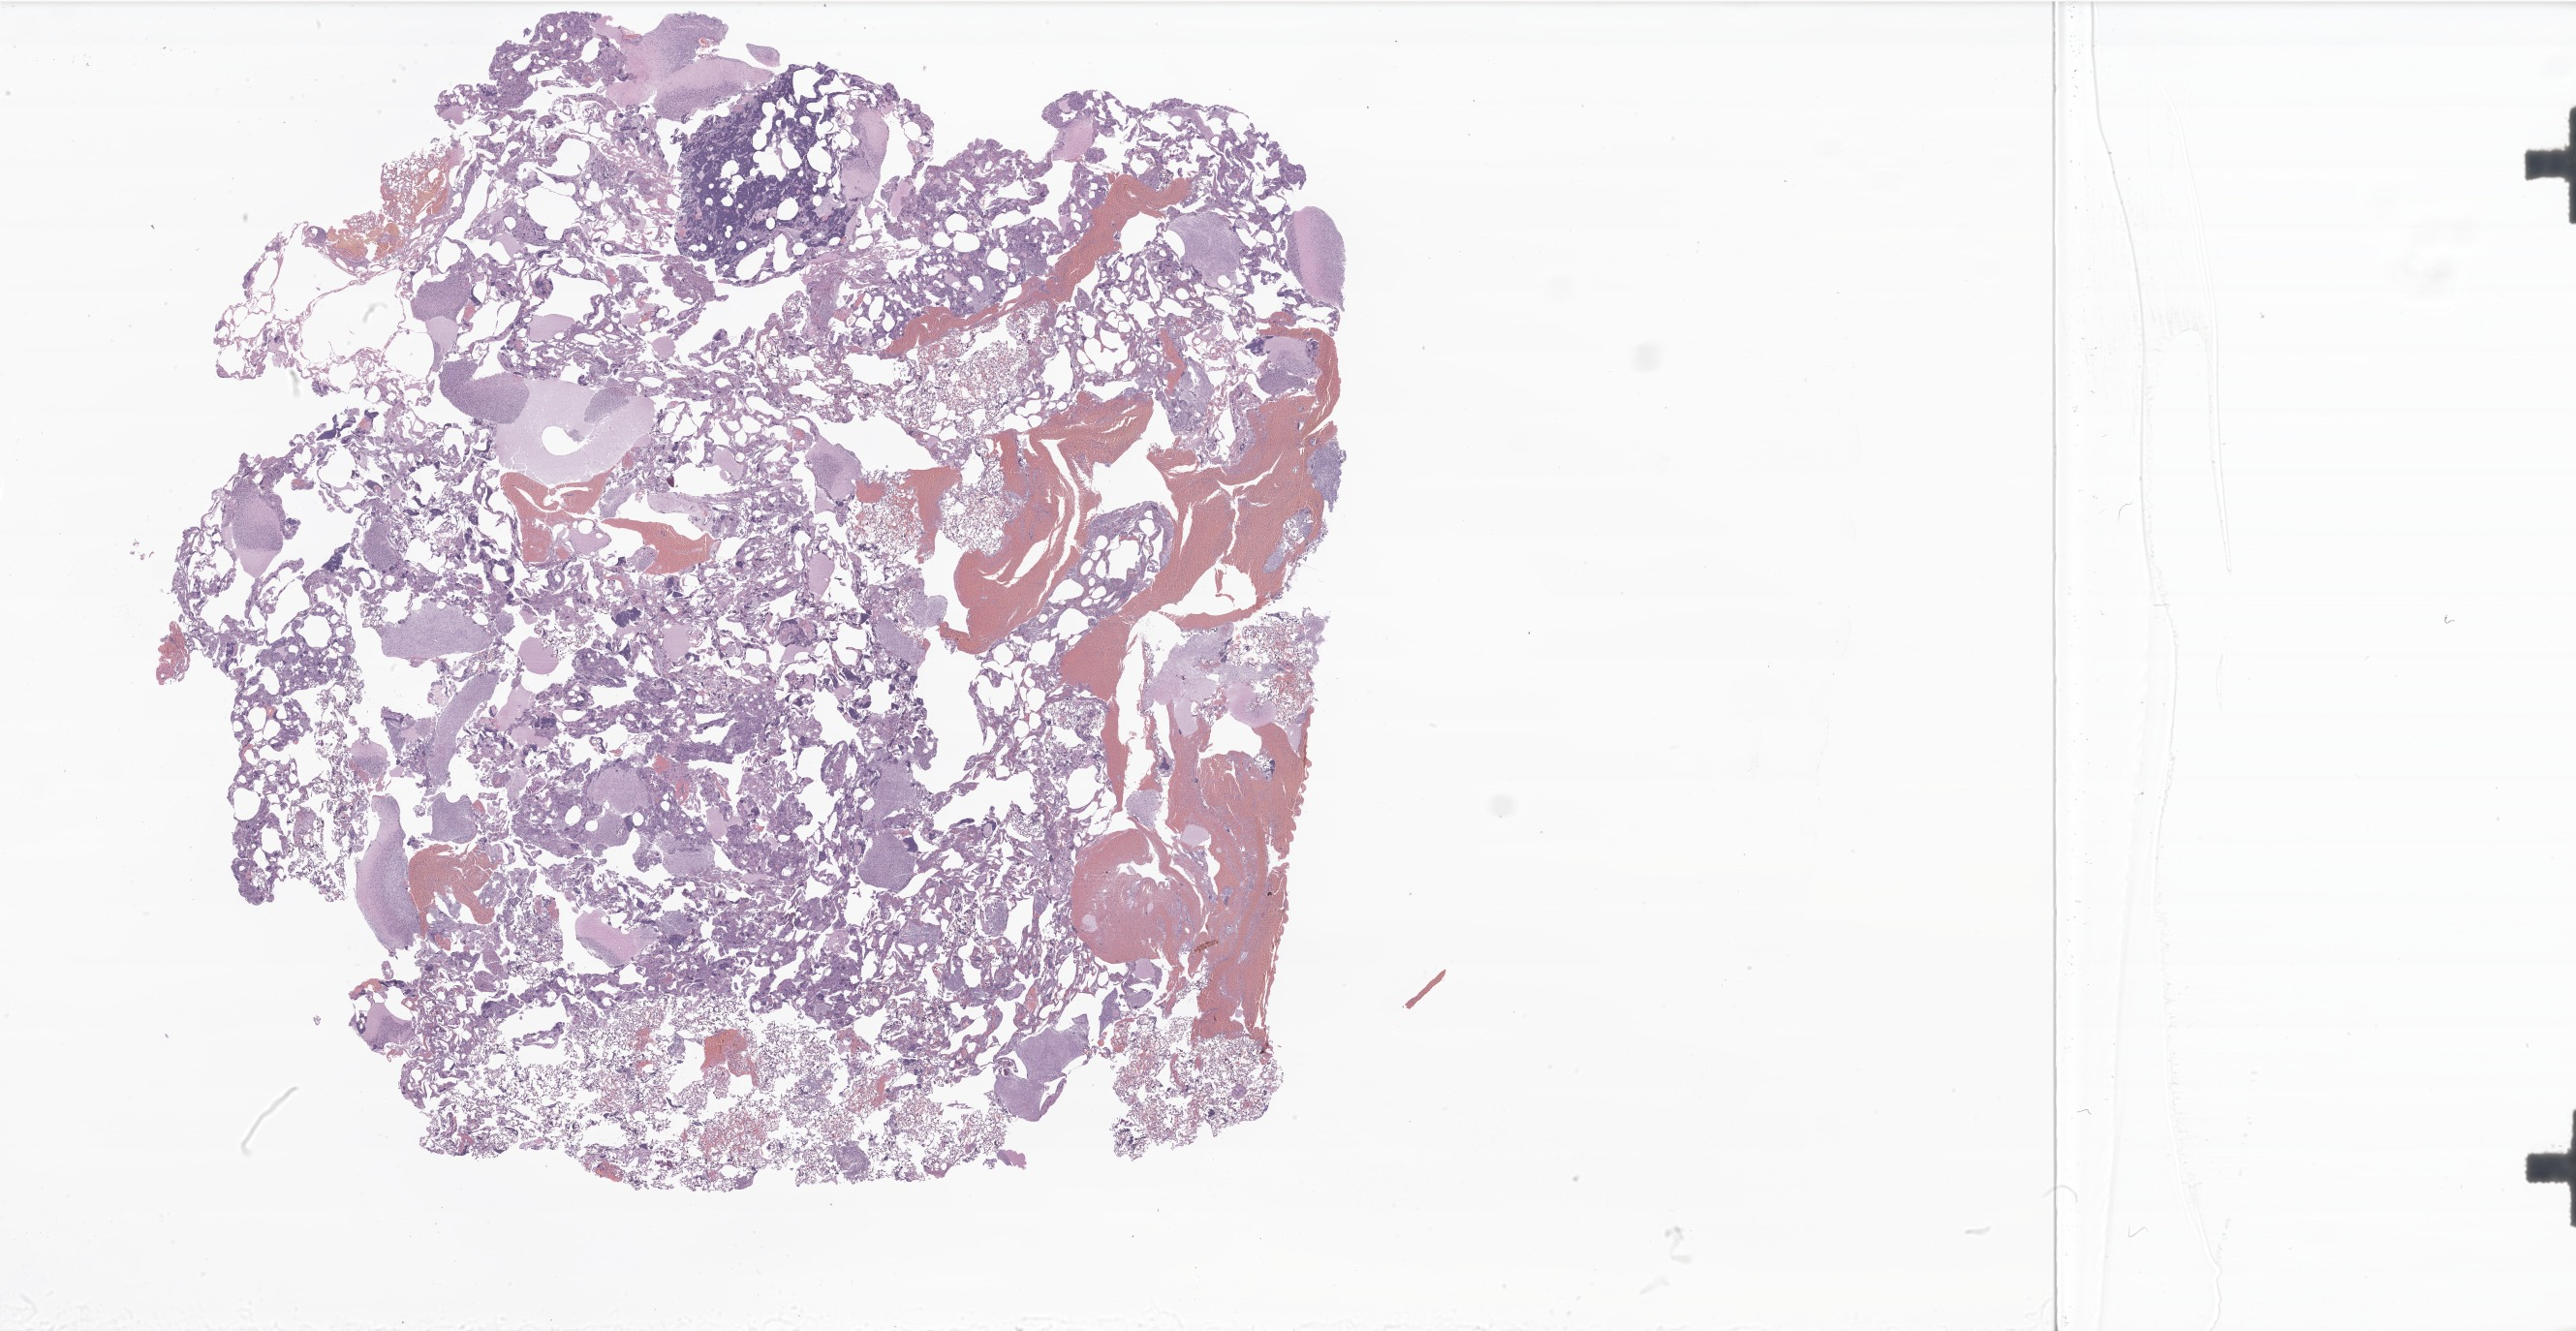
Hematoxylin and eosin (H&E) whole-slide image of tumor tissue from the cerebellum — a low-resolution overview of the entire scanned area, about 44.8 x 23.2 mm. Formalin-fixed, paraffin-embedded (FFPE) tissue. Male patient, age 156 months (13 years).
Recorded diagnosis: Medulloblastoma, NOS.